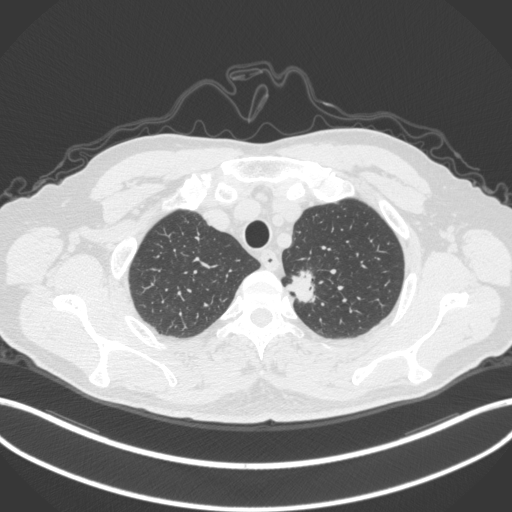
Chest CT, one axial slice. Slice 321 of 382 in the series (ordered by position). 120 kVp. Lung window (W 1500 / L -600 HU). 512 × 512 image matrix, field of view 400 × 400 mm. Patient: male, 64 years. From the clinical record (not read from this slice): clinical TNM (as recorded): T1c N0 M0.
Outlined on this slice (rectangle marked by the reading radiologist):
- lung tumour (recorded histology: adenocarcinoma): bounding box <284,261,323,312> (left, top, right, bottom; pixels)